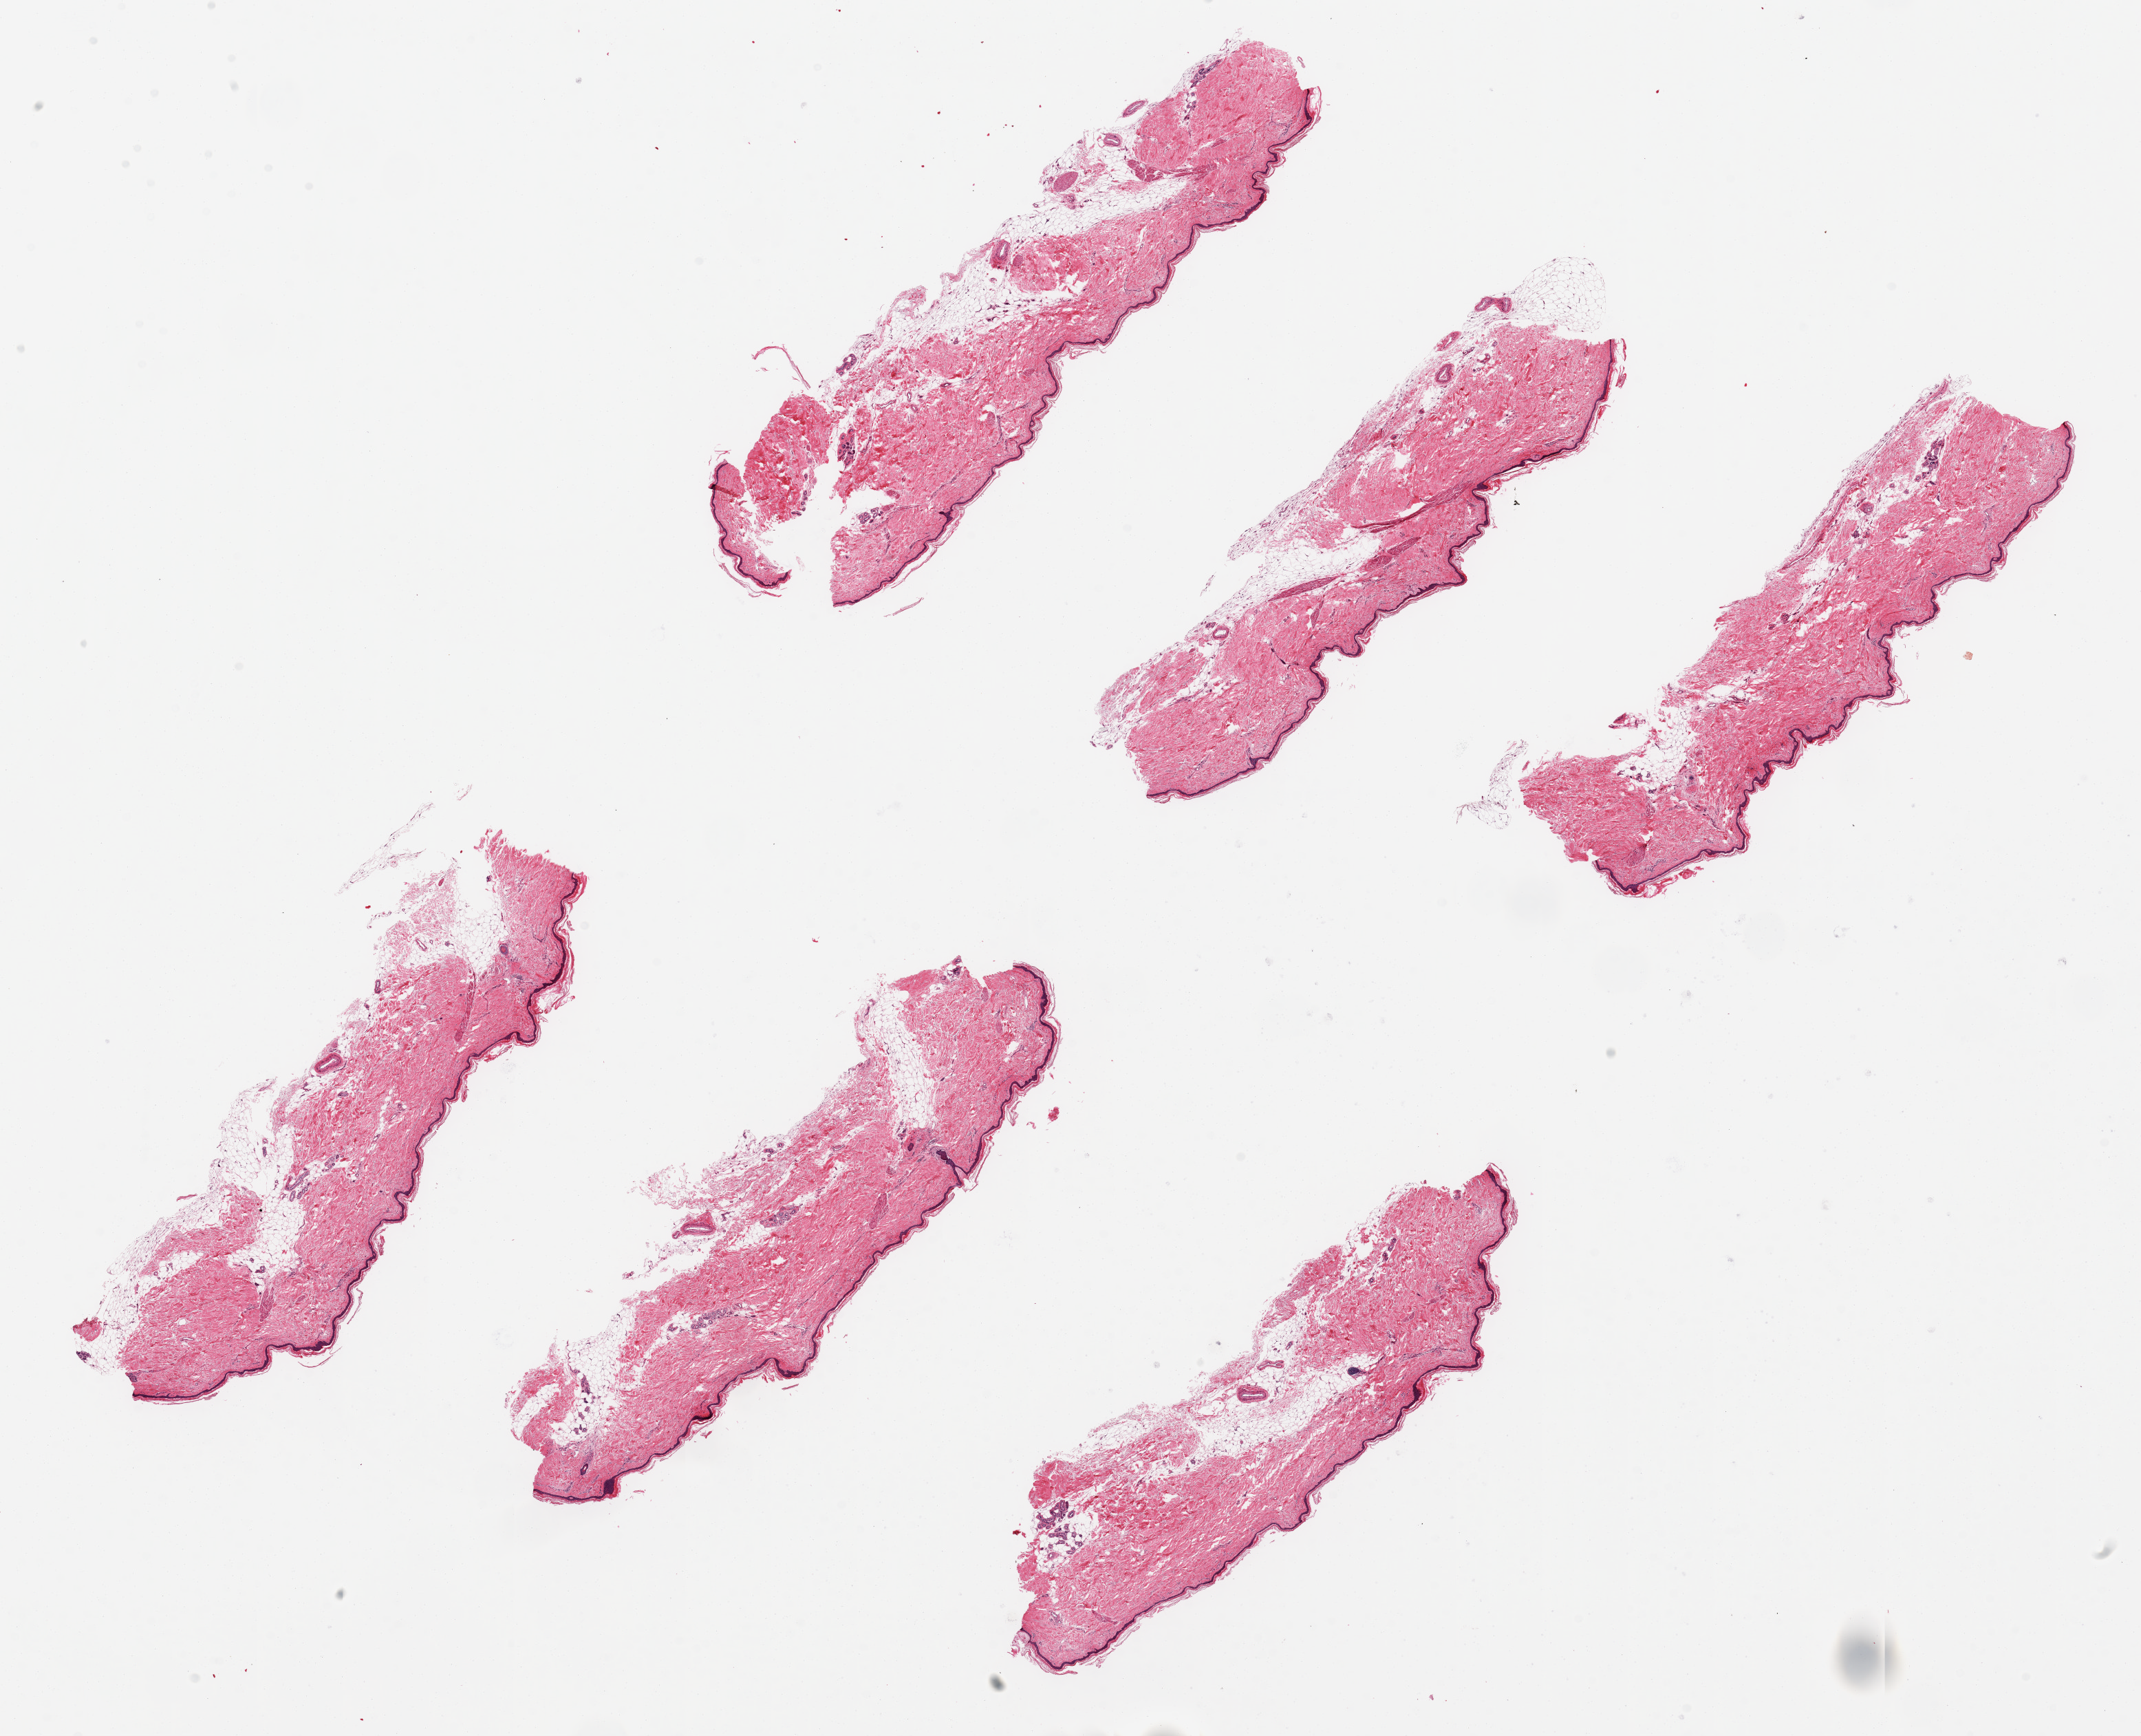
Whole-slide image, haematoxylin and eosin stain, brightfield — whole scanned area (about 24.6 x 20.0 mm, acquisition: 20x scan) shown as a low-resolution overview; PAXgene-fixed paraffin-embedded (PFPE) section; section of skin of lower leg (target tissue); donor tissue sample. Donor: female.
Reviewer comment on this tissue sample: 6 pieces up to 8.6x2.2 mm.